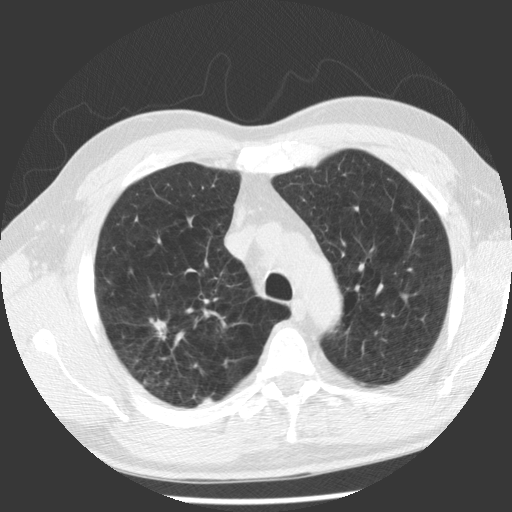
Low-dose screening chest CT, one axial slice; slice 86 of 112 in the series (ordered by position); reconstruction kernel STANDARD; lung window (W 1500 / L -600 HU); 2.5 mm slice thickness; 512 × 512 image matrix, field of view 344 × 344 mm.
Structures marked on this image (manually delineated by an expert):
- lesion 1 (tumor, upper lobe of right lung): bounding box (x1, y1, x2, y2) in pixels: (150, 318, 166, 331)